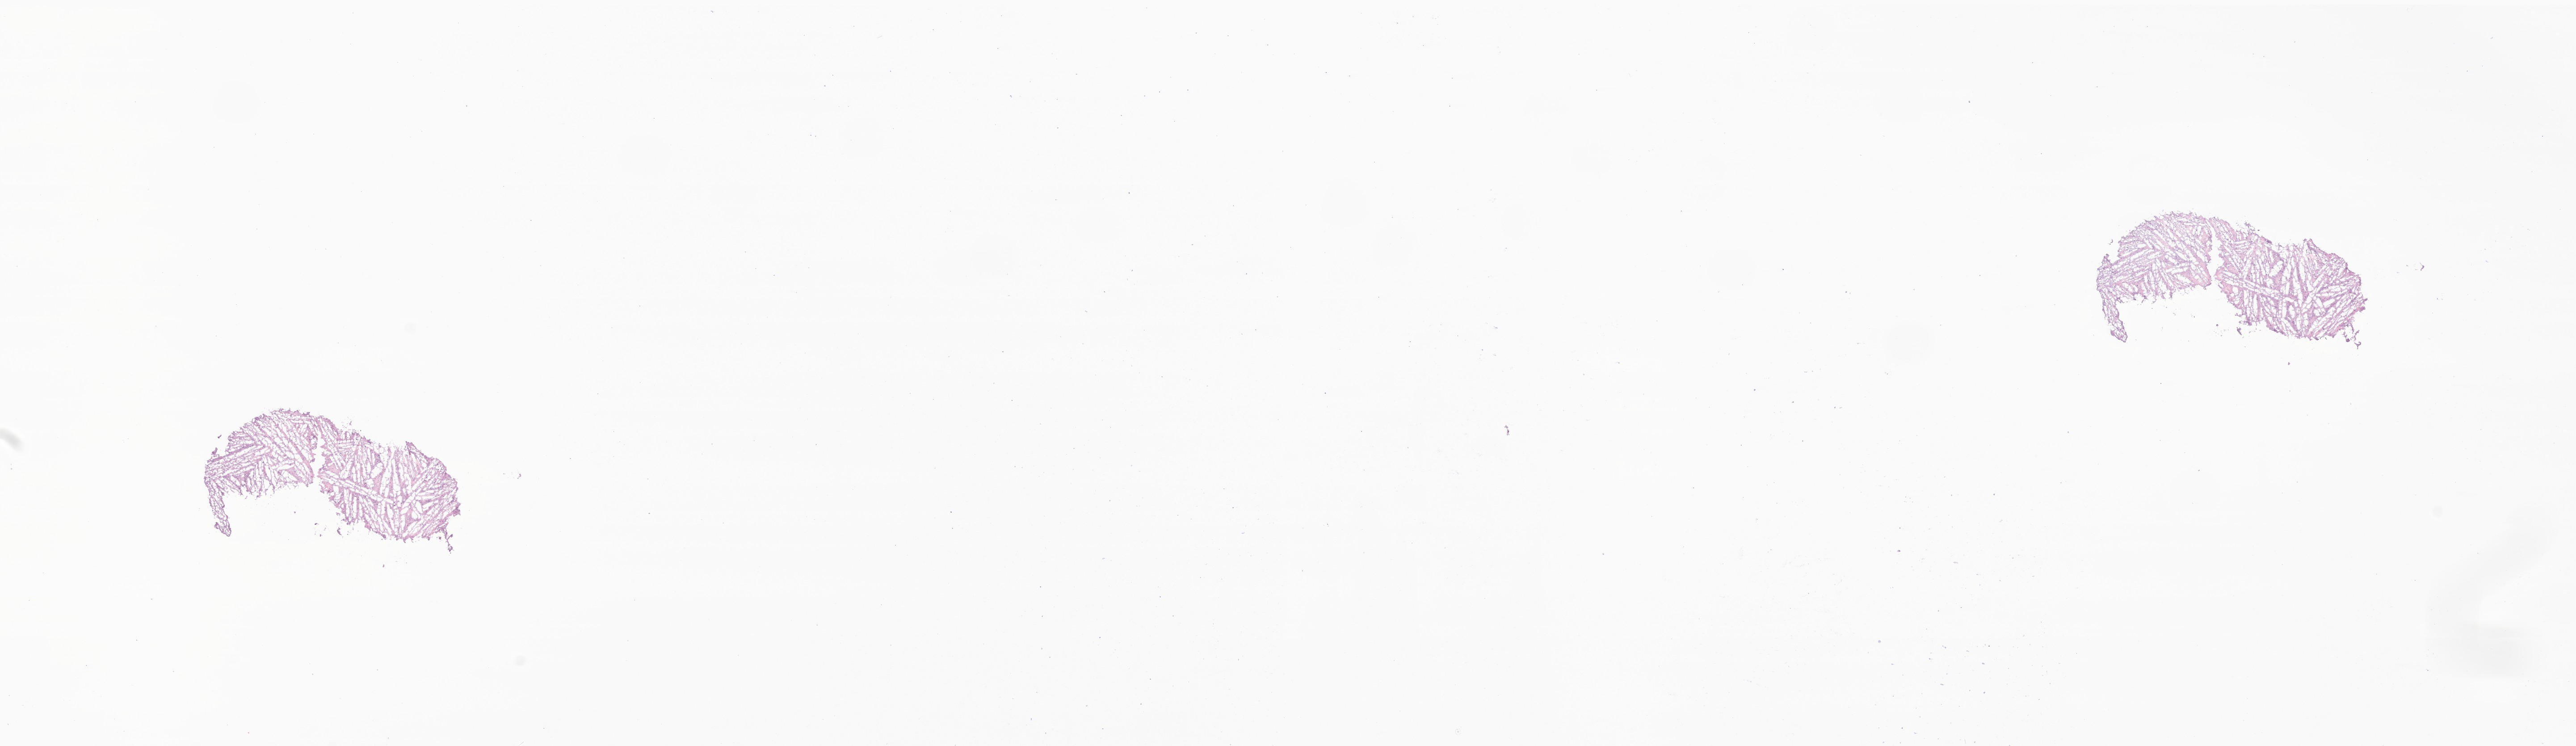
Haematoxylin and eosin whole-slide image of tumor tissue from the brain, a low-resolution overview of the entire scanned area, about 24.3 x 7.0 mm. Cryosection (OCT / tissue freezing medium). Patient: female, age 123 months.
Recorded diagnosis: Glioma, malignant.